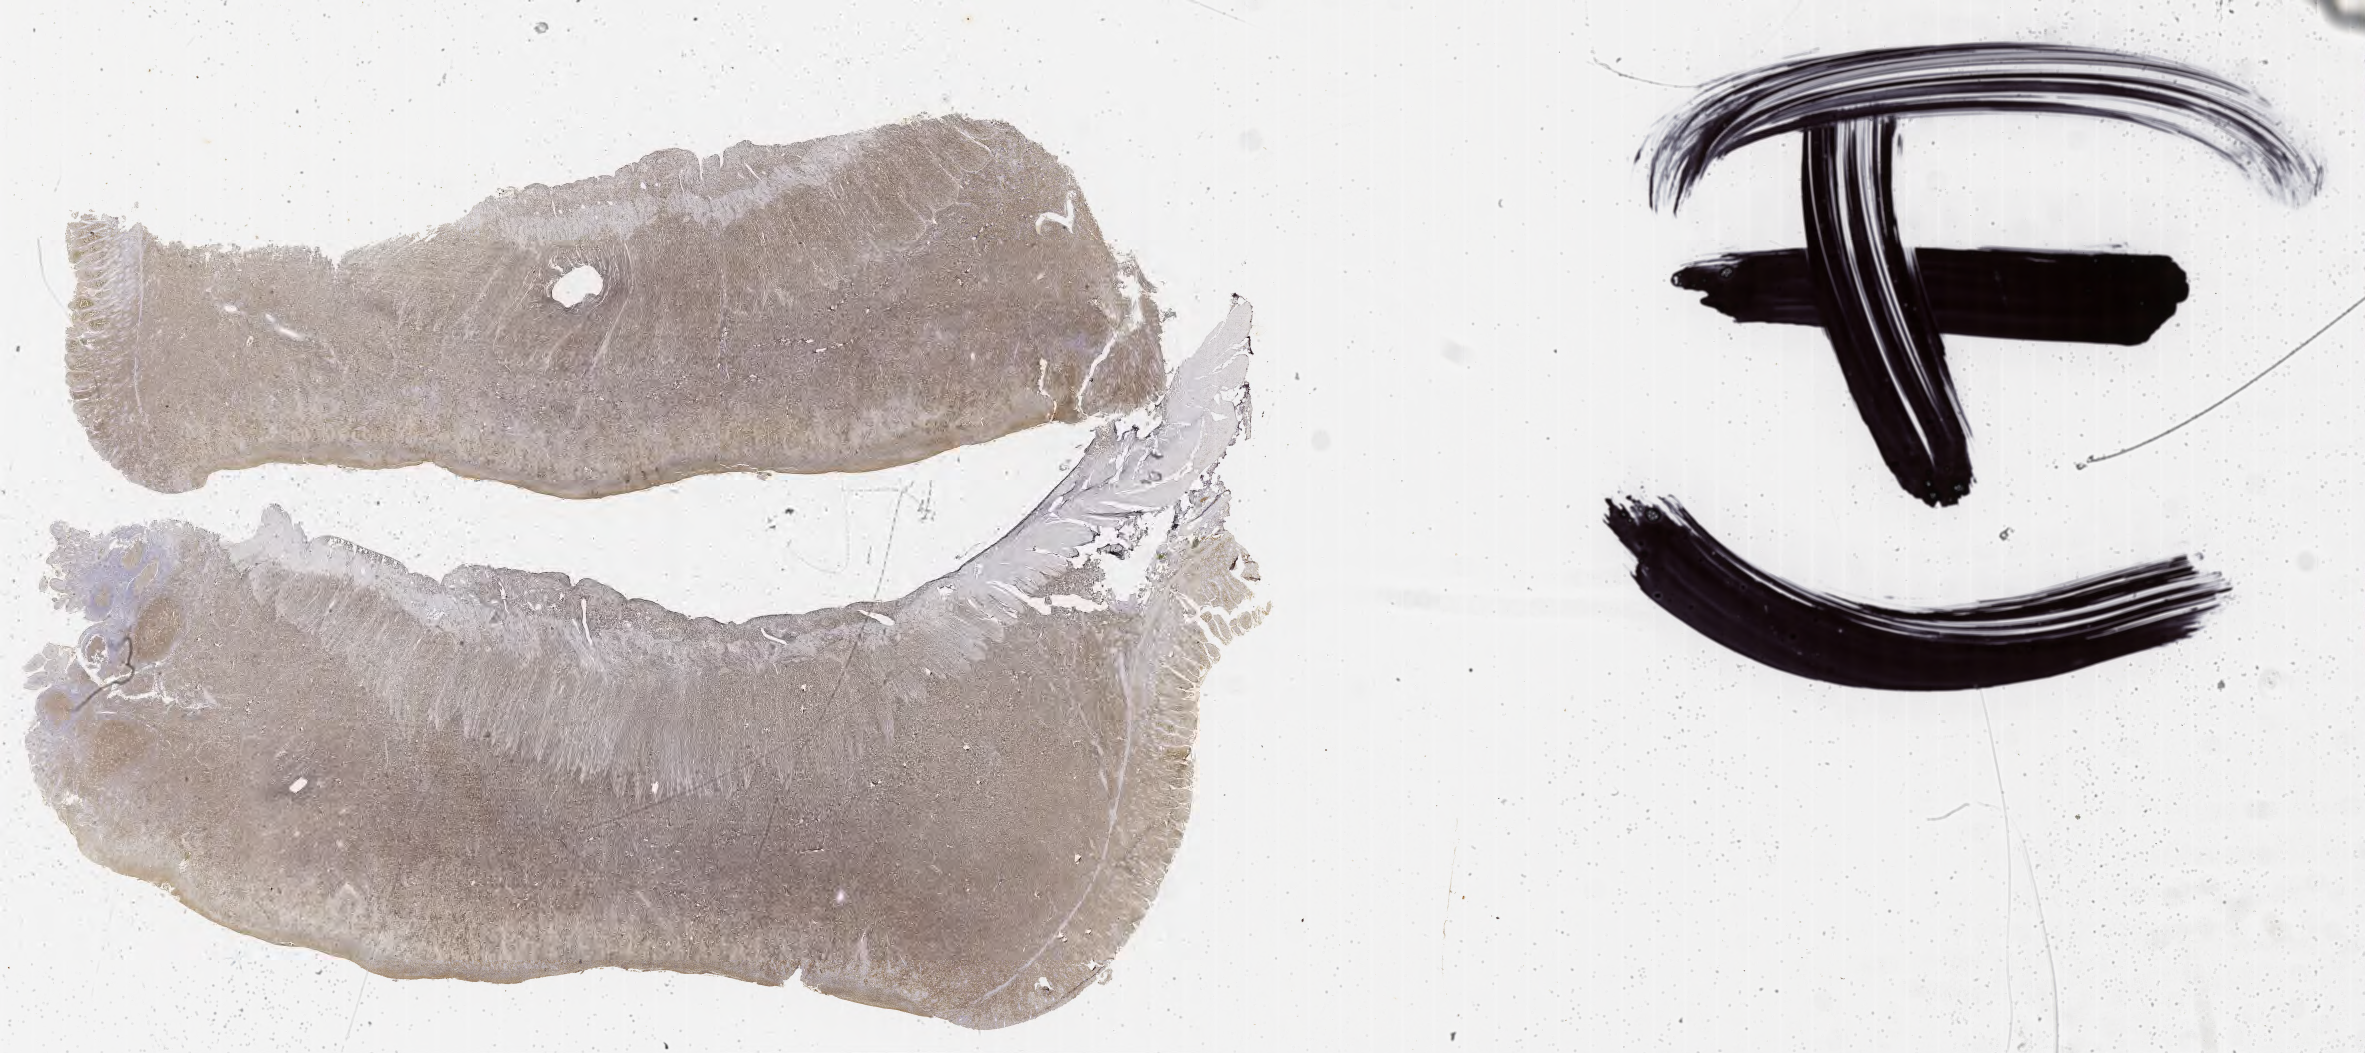
IHC for CD10, whole-slide image — whole scanned area (about 38.2 x 17.0 mm) shown as a low-resolution overview; specimen: tumor tissue. Patient female; aged 27.
Diagnosis: Burkitt lymphoma, NOS.